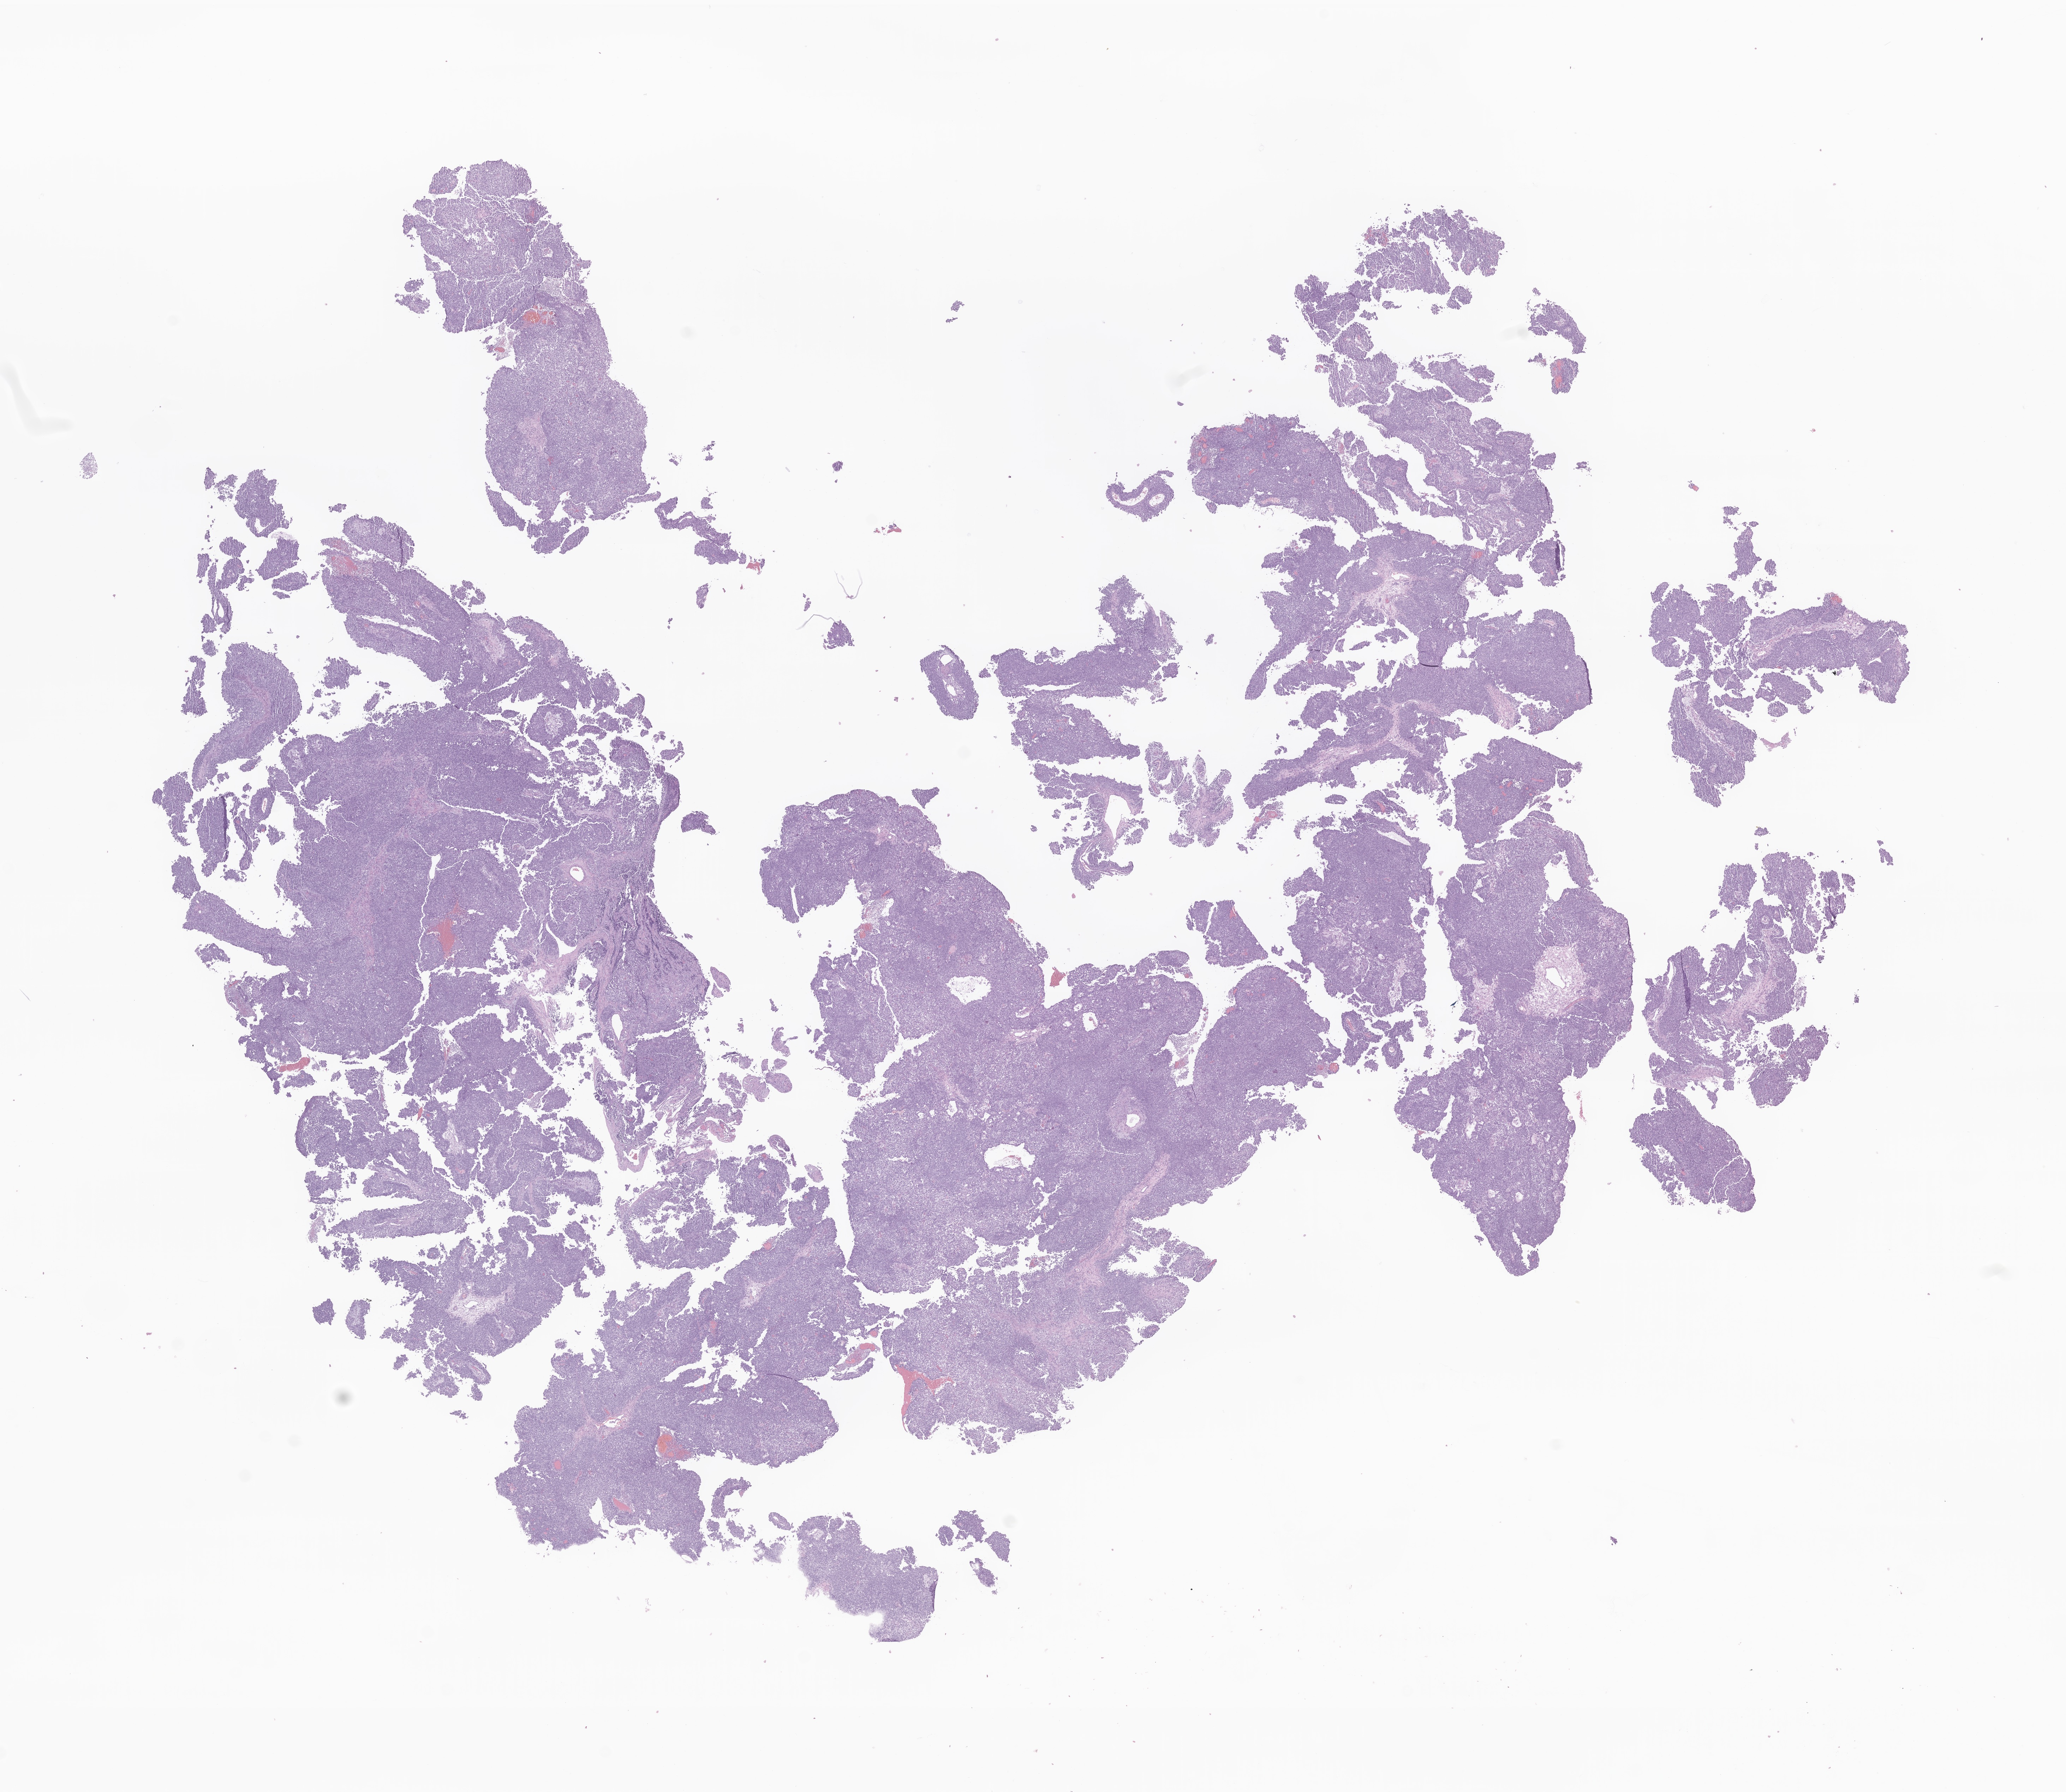
Digitized H&E-stained section of tumor tissue from the brain — a low-resolution overview of the entire scanned area, about 24.7 x 21.4 mm; formalin-fixed paraffin-embedded section. Patient: female, age 517 days (about 1.4 years).
Diagnosis: Neoplasm, malignant.